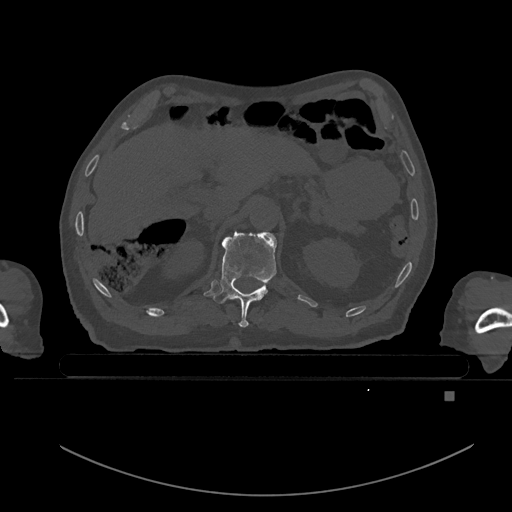
CT including the spine, one axial slice. Slice 22 of 969 in the series (ordered by position). Bone window (W 1800 / L 400 HU). 0.5 mm slice thickness. 512 × 512 image matrix, field of view 456 × 456 mm. Patient: male, 82 years. Case-level facts recorded for this patient, not image findings: primary cancer: prostate; vertebrae with lytic lesions (as recorded): T11, T9, T8, T2.
Outlined on this slice (semi-automatic segmentation, software-assisted and operator-edited):
- T11 vertebra: box from (x=213, y=232) to (x=277, y=328) px